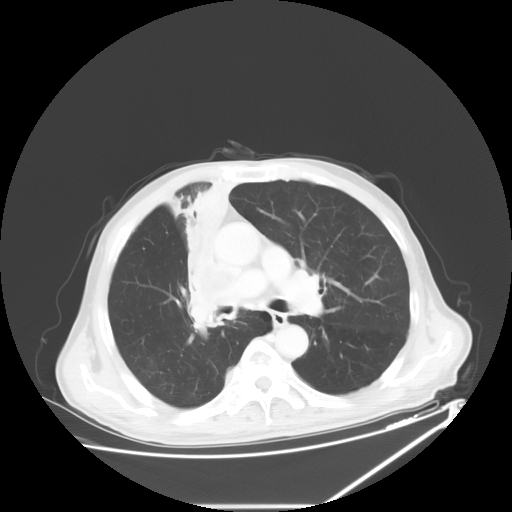
Chest CT, one axial slice; position 38 of 60 along the scan axis; reconstruction kernel STANDARD; lung window (W 1500 / L -600 HU); 5 mm slice thickness; 512 × 512 image matrix. Patient: male, 73 years. Case-level facts recorded for this patient, not image findings: clinical TNM (as recorded): T2a N1 M0.
Structures marked on this image (rectangle marked by the reading radiologist):
- lung tumour (recorded histology: squamous cell carcinoma): bounding box <166,171,245,330> (left, top, right, bottom; pixels)